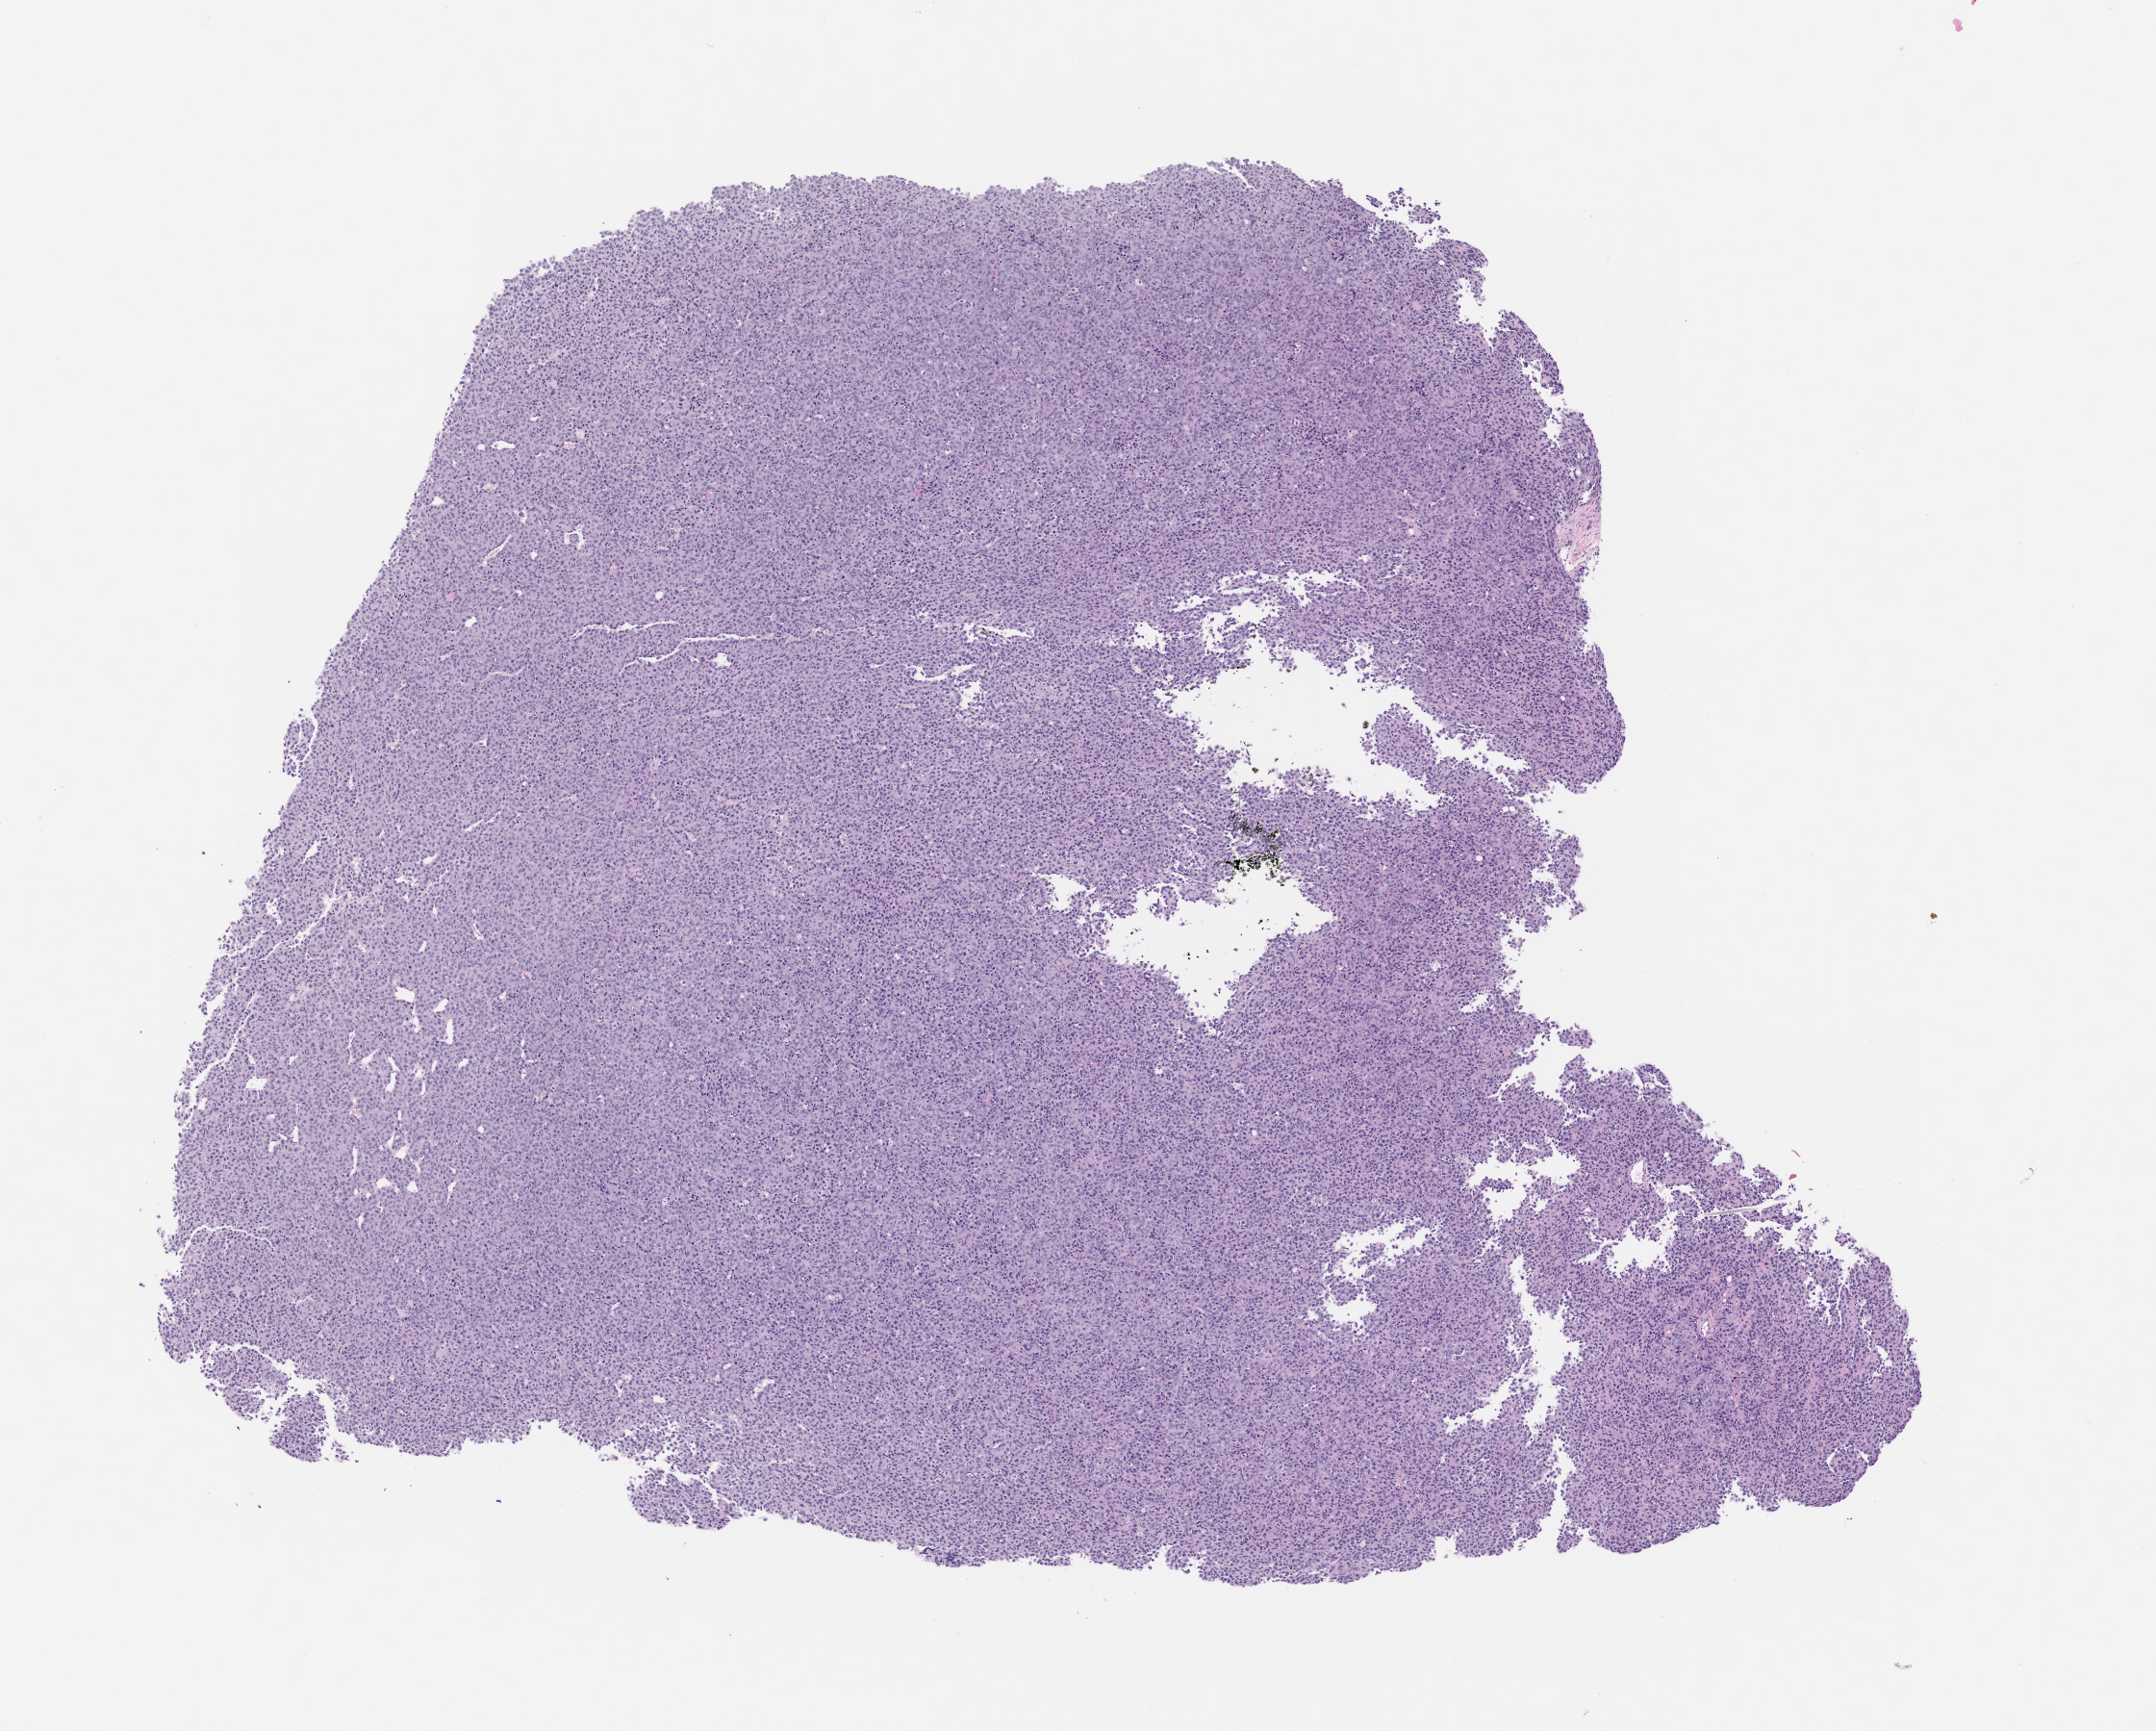
H&E whole-slide image of a patient-derived xenograft (PDX) tumor grown in a mouse, passage 2, low-resolution overview of the scanned area, about 9.0 x 7.2 mm. Formalin-fixed paraffin-embedded section. Originating tumor site category: bone.
• originating patient diagnosis: Osteosarcoma